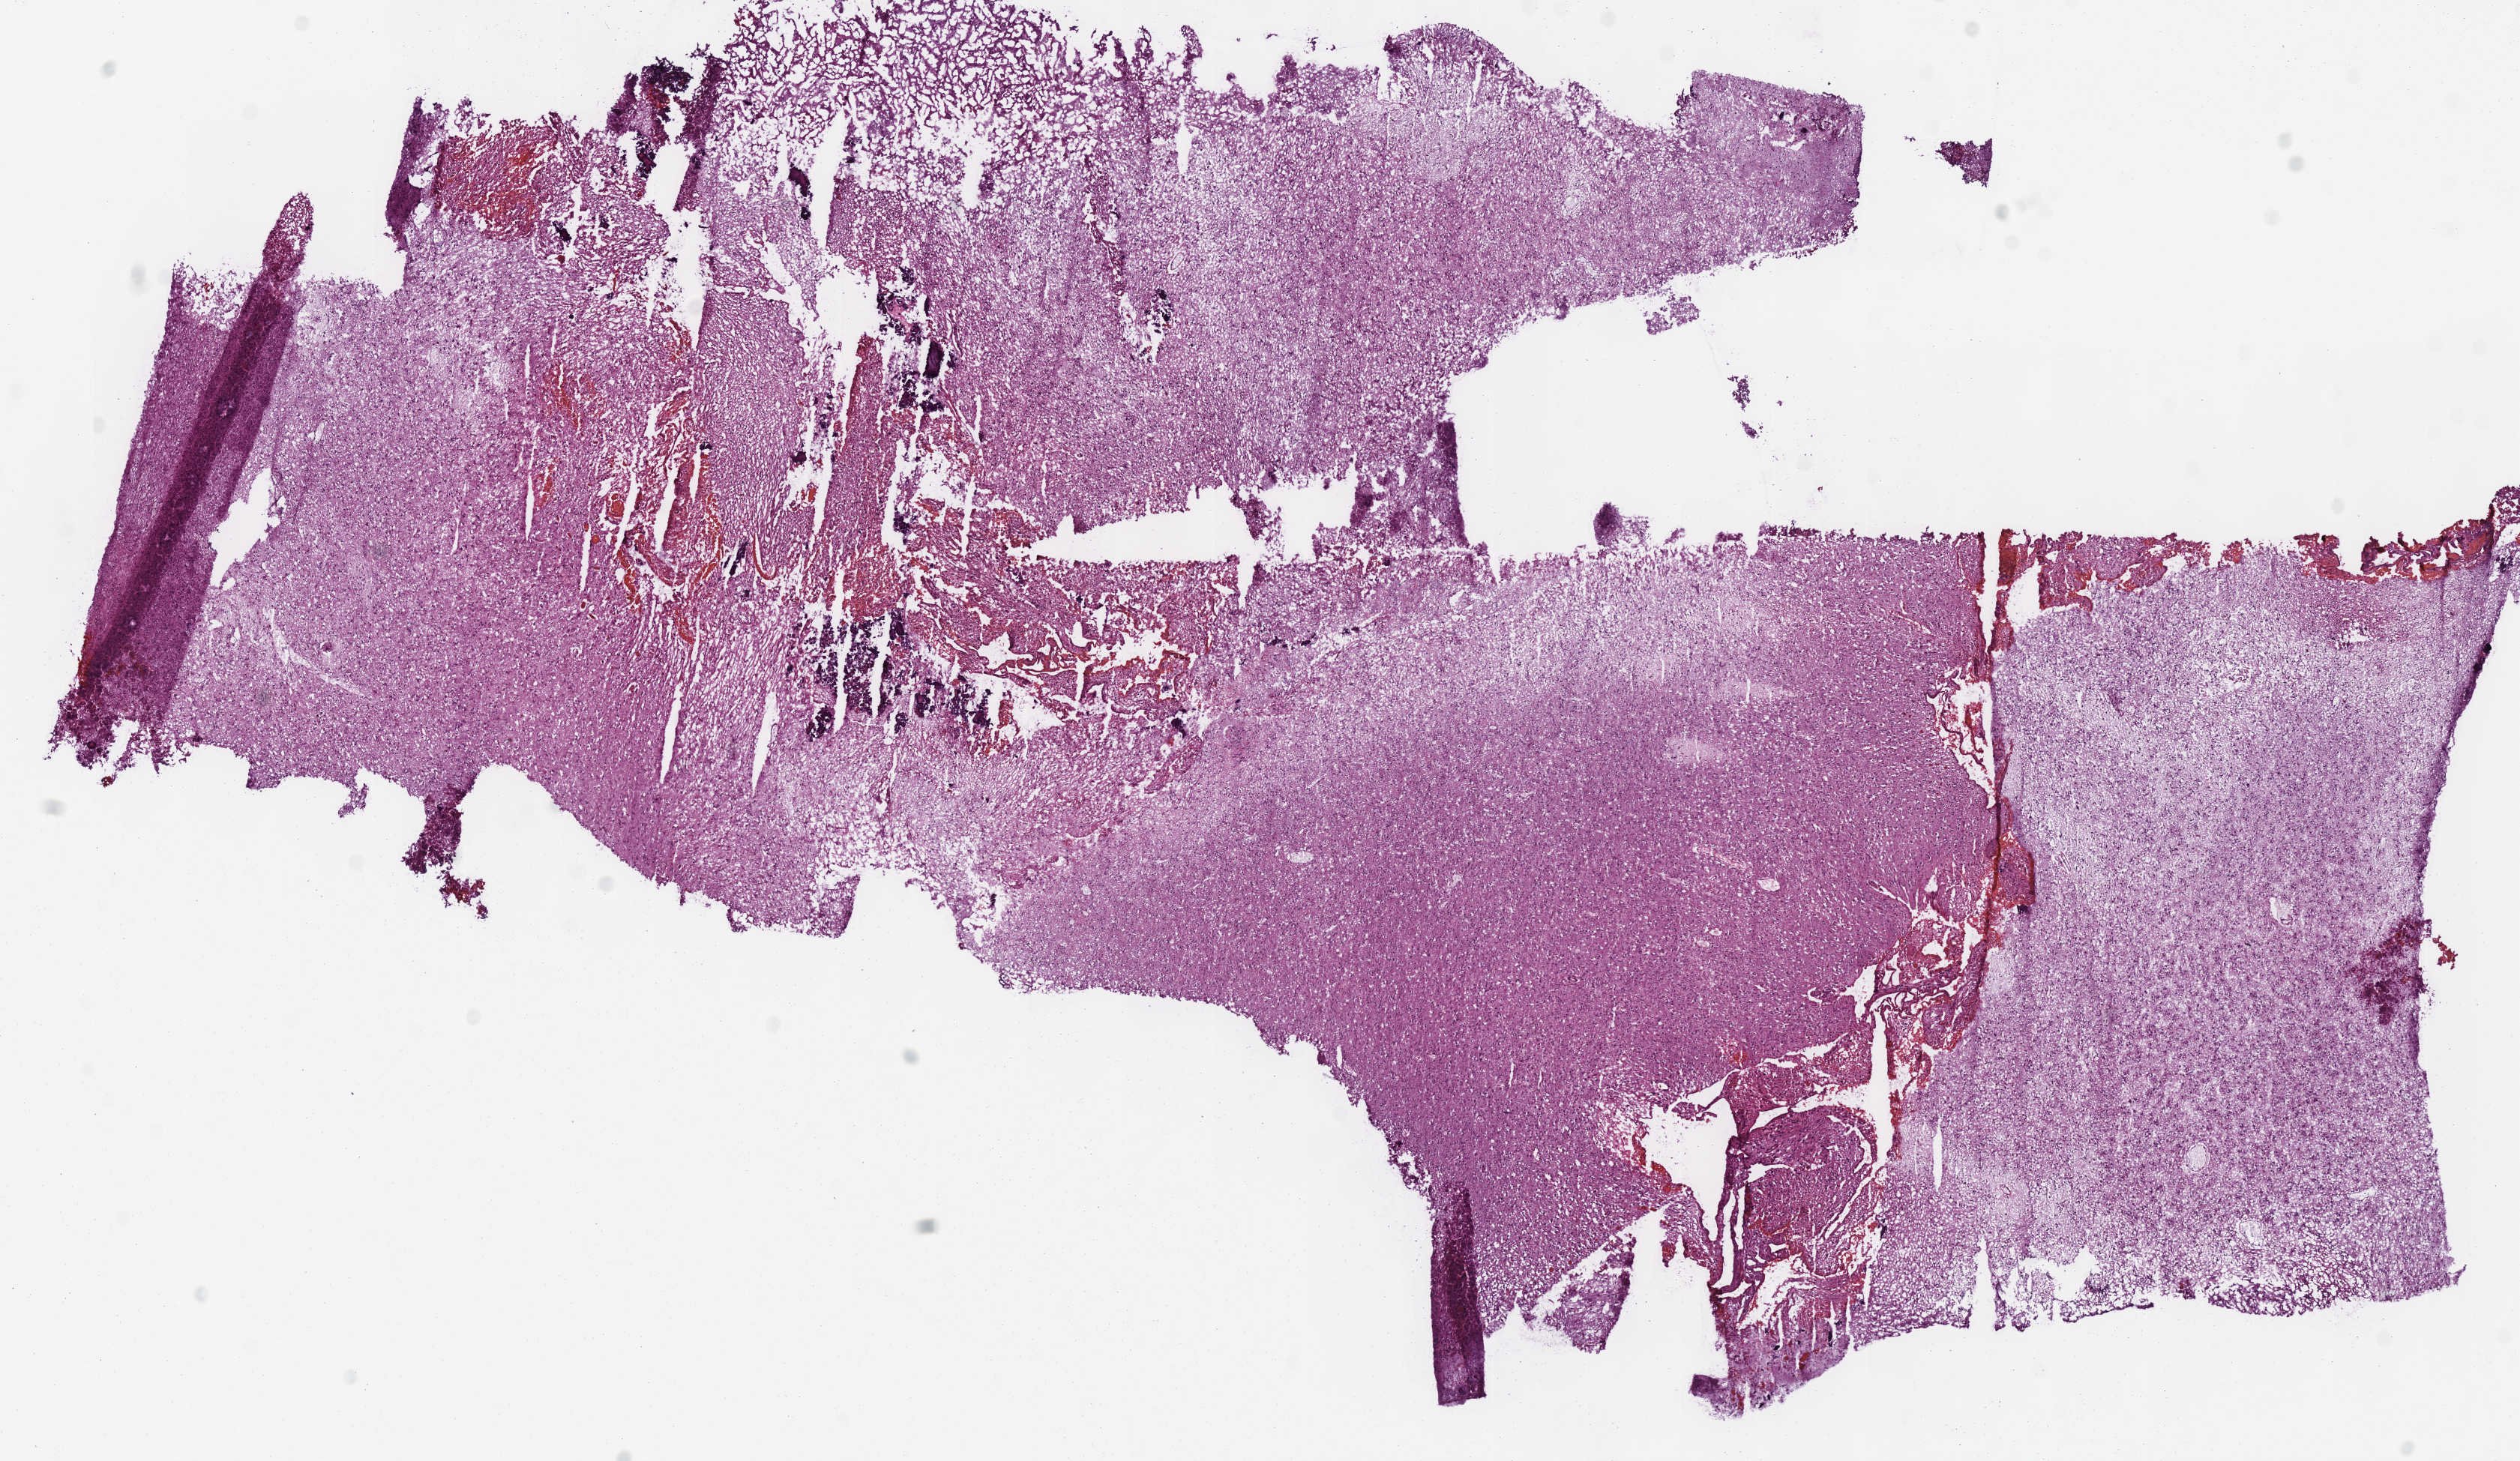
Digitized Hematoxylin and eosin (H&E) stained tissue section (whole slide) — shown as a low-resolution overview of the whole scanned area (about 13.2 x 7.7 mm), frozen section from the top of the tissue portion, primary tumour sample from the brain. Male patient; age at initial diagnosis 57 years. Histologic grade: G3 (poorly differentiated). Slide review estimates, as recorded: tumour cells 100%, tumour nuclei 75%, normal cells 0%, stromal cells 0%, necrosis 0%.
- pathologic diagnosis: Astrocytoma, anaplastic (cerebrum)